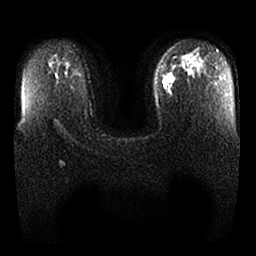
Breast MRI, one axial slice; position 16 of 25 along the scan axis; diffusion-weighted series; image 2 of 4 stored at this slice position (different b-values; order by instance number); 1.5 T; 4 mm slice thickness; 256 × 256 image matrix, field of view 340 × 340 mm. Female patient.
Outlined on this slice (manually delineated by an expert):
- tumour on diffusion-weighted imaging: box from (x=162, y=72) to (x=177, y=89) px